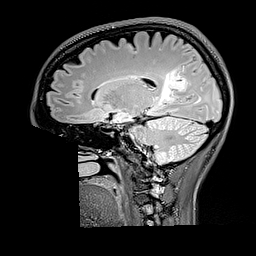
Brain MRI from a brain-tumour surgery series, one sagittal slice. Position 102 of 176 along the scan axis. T2 FLAIR. 1 mm slice thickness. 256 × 256 image matrix, field of view 256 × 256 mm. Case-level facts recorded for this patient, not image findings: histopathology: Oligodendroglioma; WHO grade: 2; IDH mutation: yes; tumour location: Right Parietal.
Annotated regions visible in this slice (outlined manually by an expert reader):
- tumour: box from (x=158, y=66) to (x=188, y=104) px